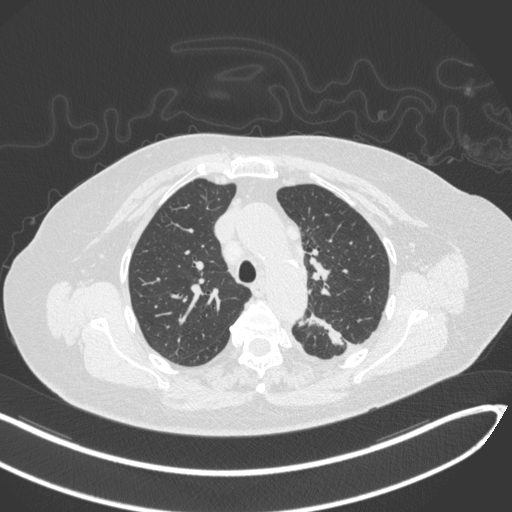
Chest CT, one axial slice; position 226 of 270 along the scan axis; reconstruction kernel B31f; lung window (W 1500 / L -600 HU); 512 × 512 image matrix. Patient: female, 76 years. From the clinical record (not read from this slice): clinical TNM (as recorded): T1c N0 M0.
Structures marked on this image (rectangle marked by the reading radiologist):
- lung tumour (recorded histology: adenocarcinoma): bounding box (x1, y1, x2, y2) in pixels: (297, 307, 345, 349)